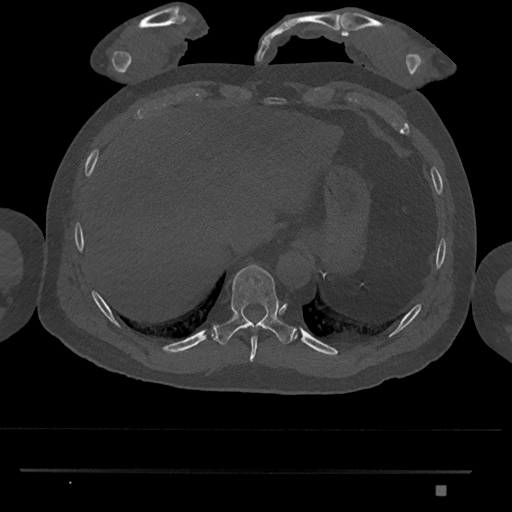
CT including the spine, one axial slice; position 1012 of 1134 along the scan axis; bone window (W 1800 / L 400 HU); 512 × 512 image matrix, field of view 429 × 429 mm. Patient: male, 65 years. From the clinical record (not read from this slice): primary cancer: prostate.
Outlined on this slice (semi-automatically segmented with operator editing):
- T10 vertebra: bounding box (x1, y1, x2, y2) in pixels: (213, 264, 295, 345)
- T9 vertebra: (249, 336, 258, 362)